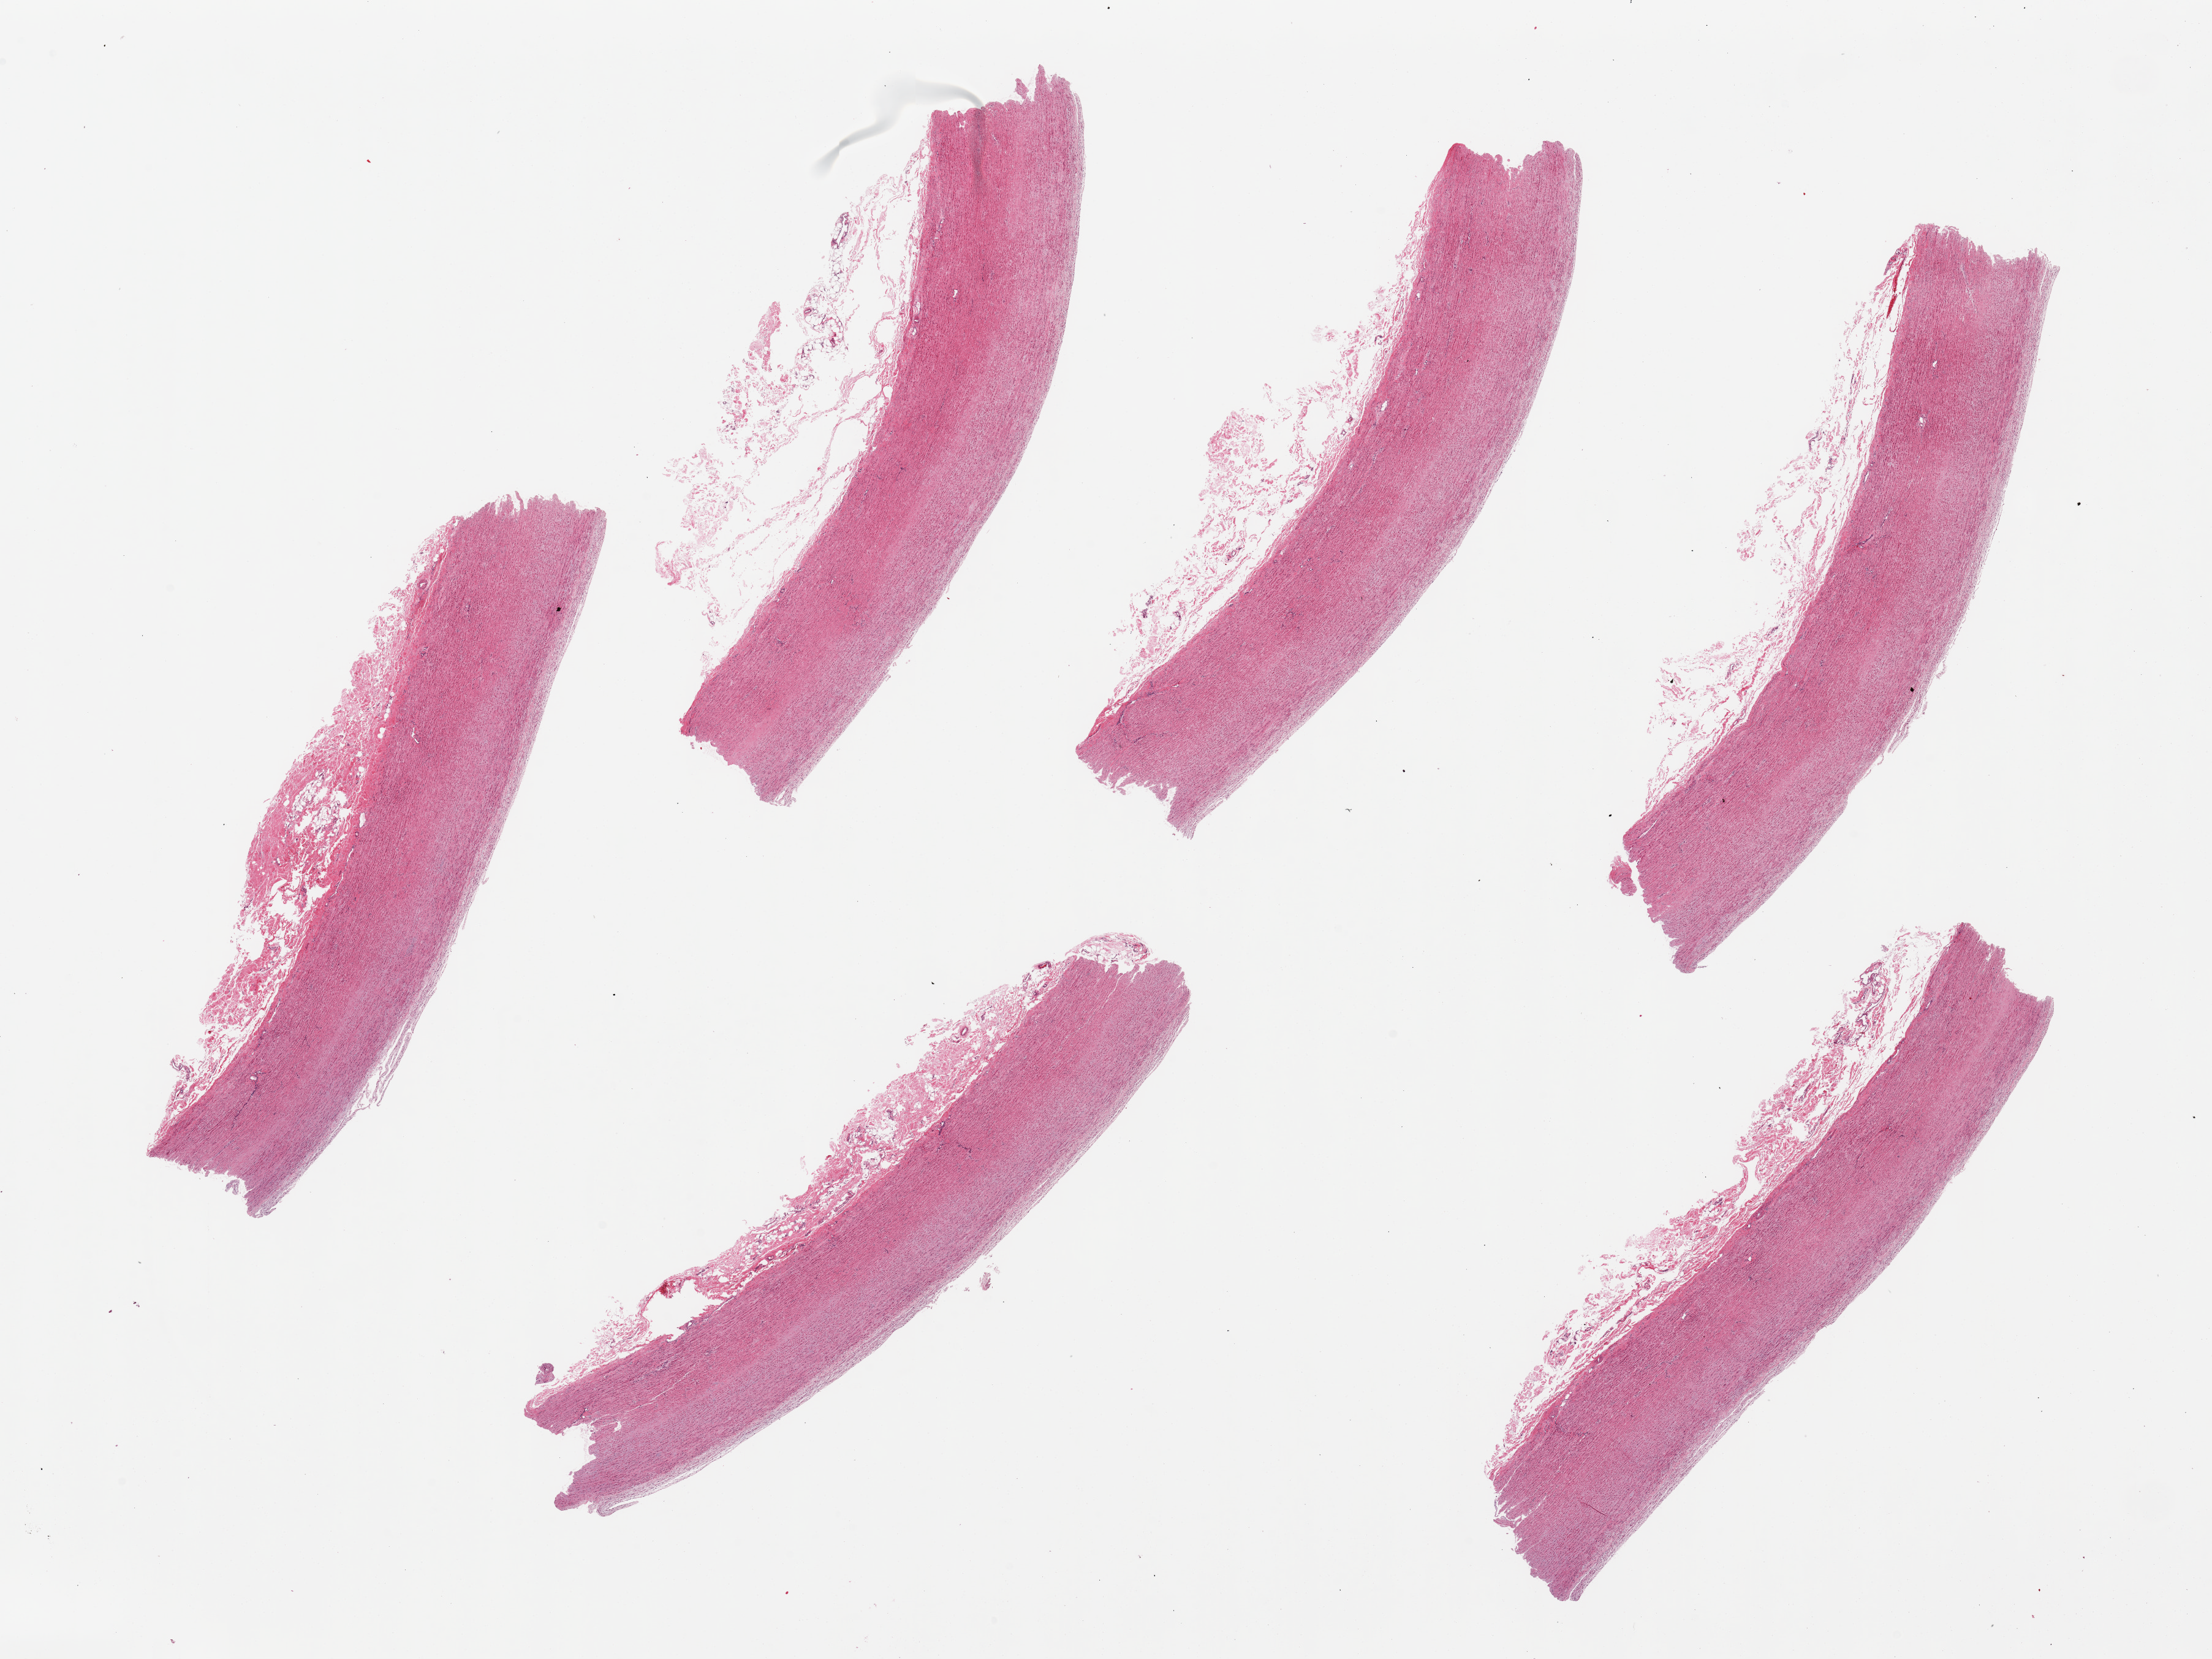
Whole-slide image, hematoxylin and eosin (H&E) stain — low-resolution overview of the scanned area, about 28.5 x 21.4 mm. PAXgene-fixed, paraffin-embedded tissue. Sampled site (target tissue): aorta. Tissue donor sample. Donor sex: male.
• pathologist's review note for this sample: 6 pieces; intimal thickening